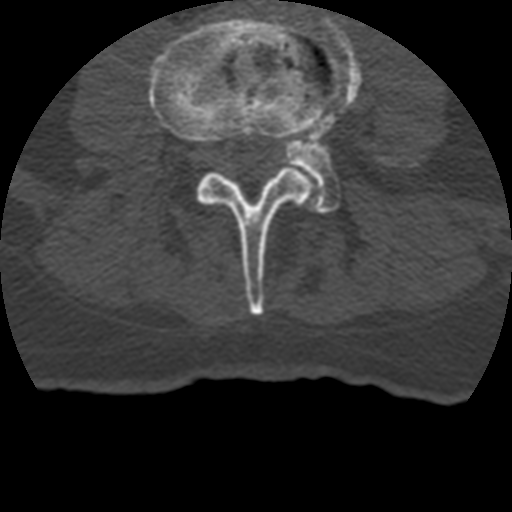
CT including the spine, one axial slice; slice 80 of 399 in the series (ordered by position); reconstruction kernel STANDARD; 120 kVp; bone window (W 1800 / L 400 HU); 1.25 mm slice thickness; 512 × 512 image matrix, field of view 160 × 160 mm. Patient age 69 years. From the clinical record (not read from this slice): primary cancer: prostate.
Annotated regions visible in this slice (semi-automatic segmentation, software-assisted and operator-edited):
- L3 vertebra: bounding box (x1, y1, x2, y2) in pixels: (148, 12, 330, 316)
- L4 vertebra: (285, 17, 419, 213)